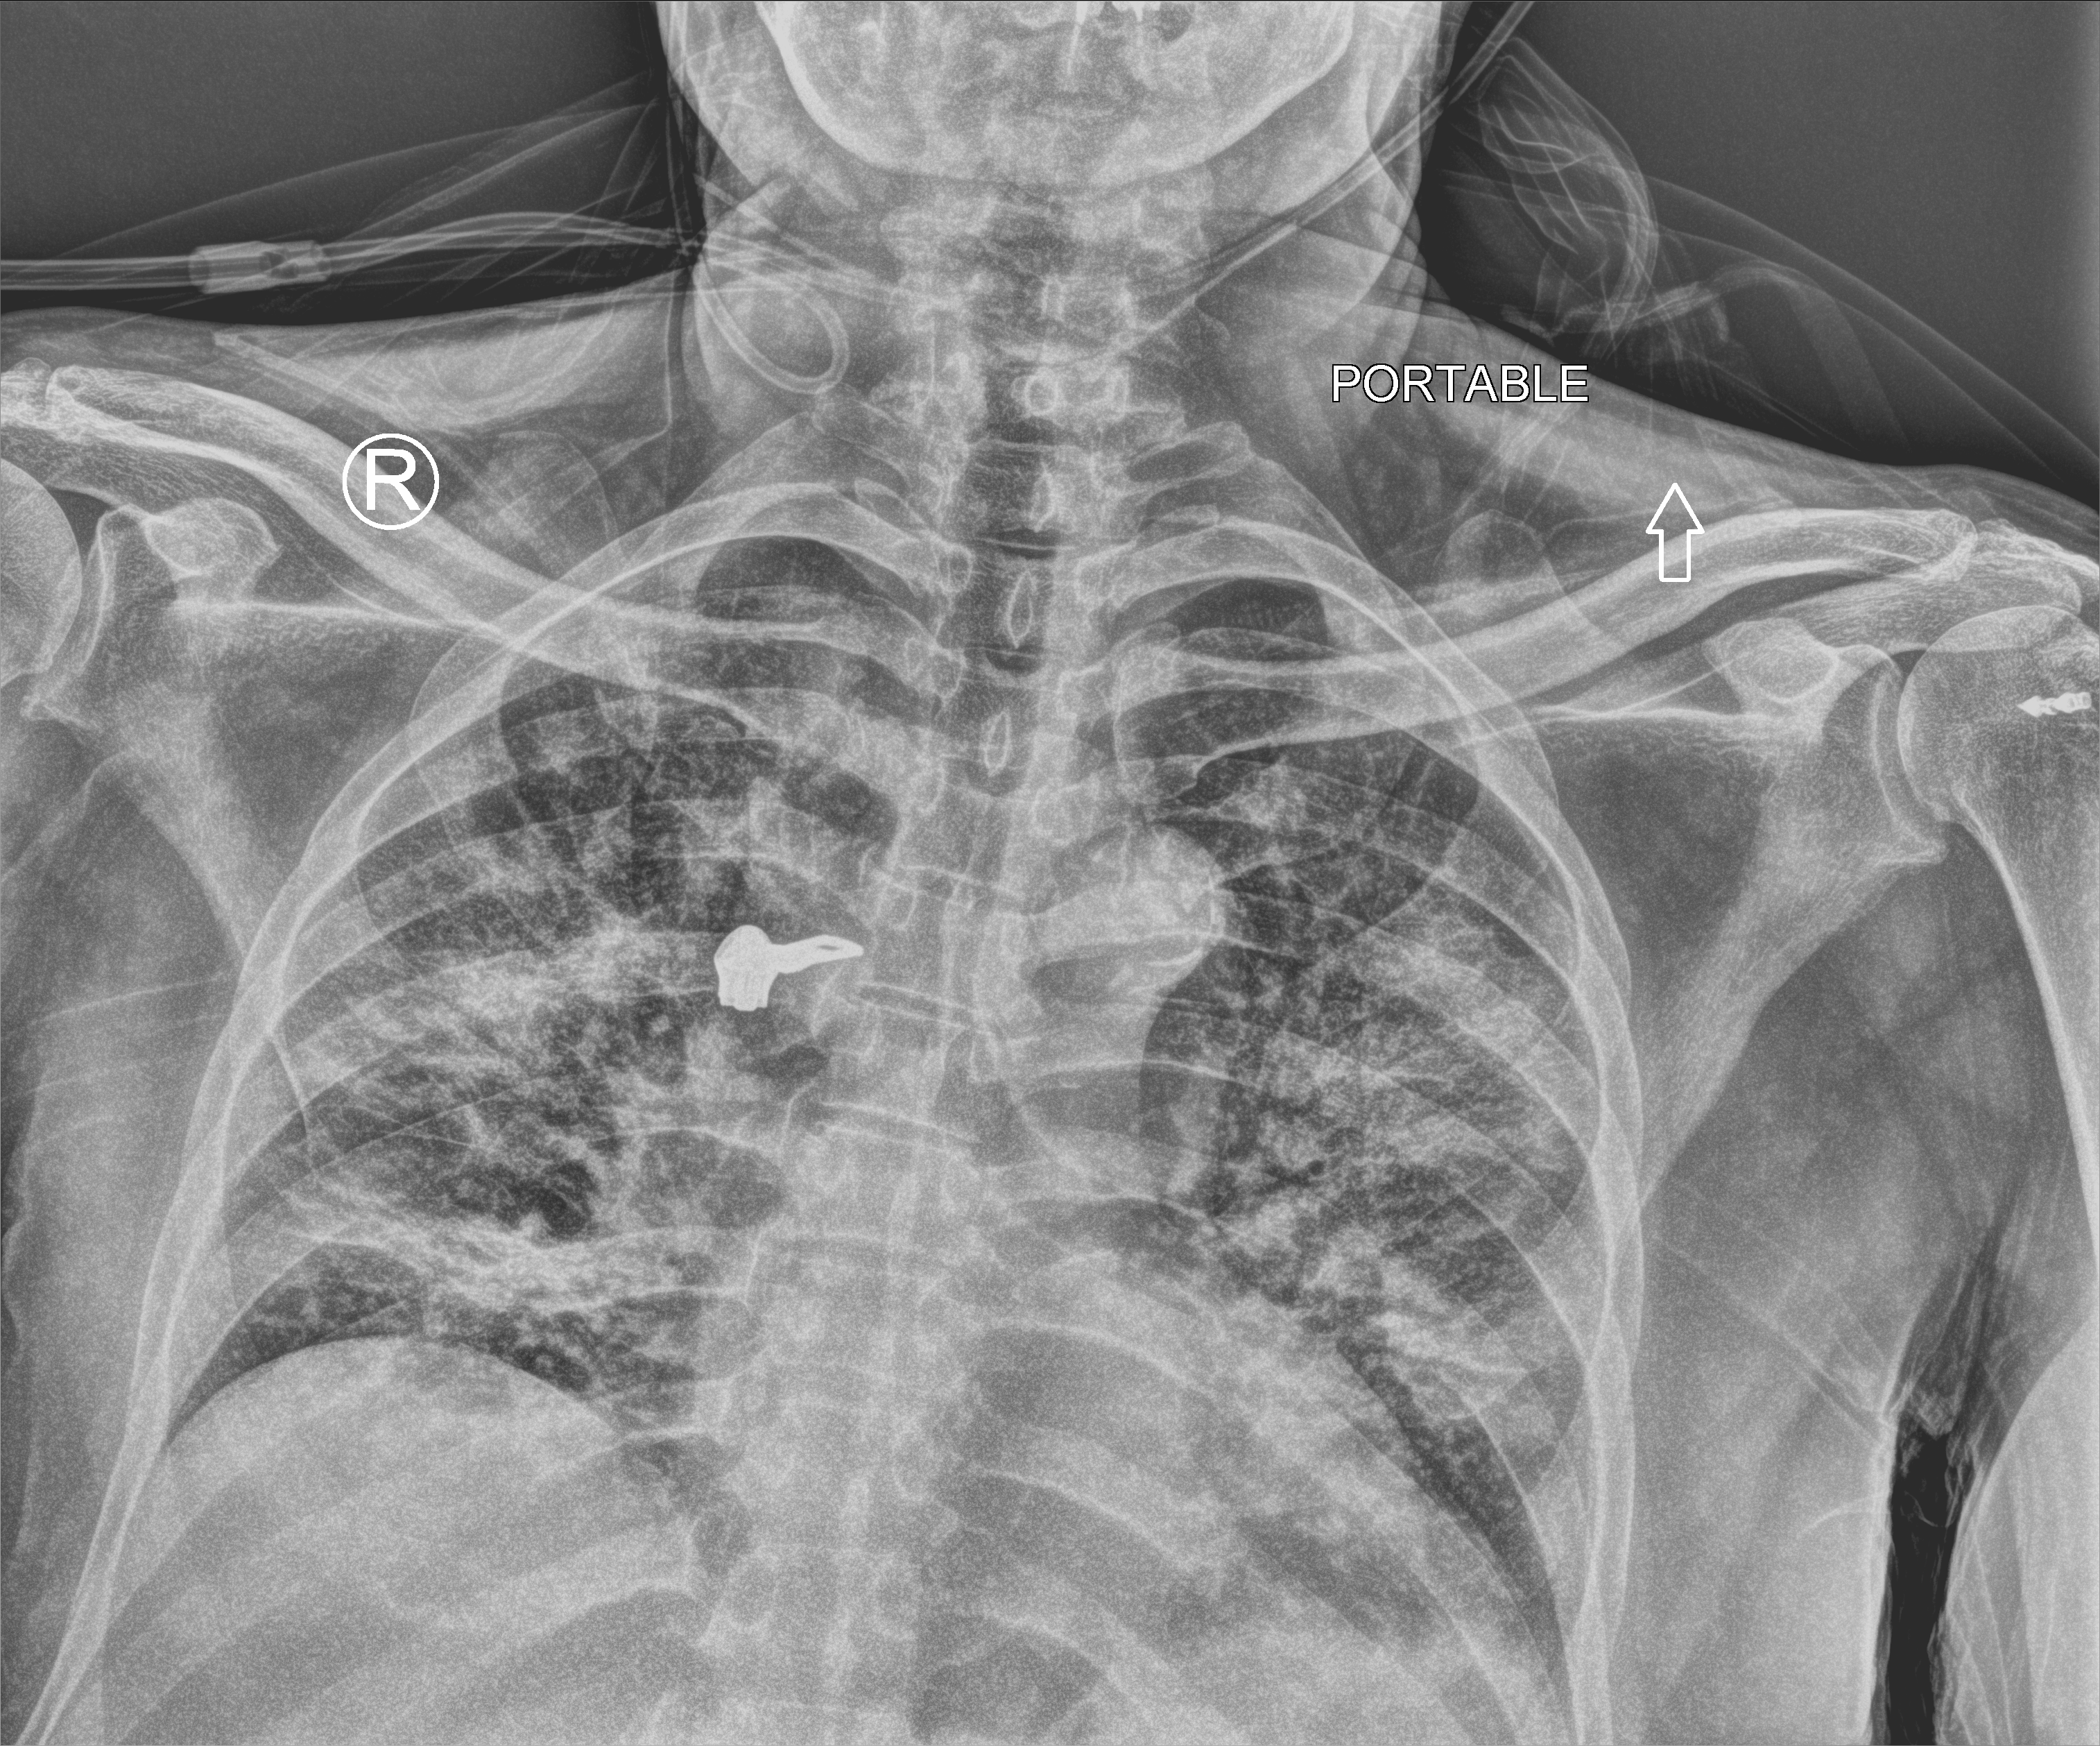
Portable chest radiograph, anteroposterior (AP) projection. Male patient hospitalised with COVID-19, age 60–74 years.
From the hospital-stay record, not from the radiograph (when in the stay this image was taken is not recorded):
- mechanically ventilated during this hospital stay: no
- length of hospital stay: 7 days
- diabetes (admission record): no